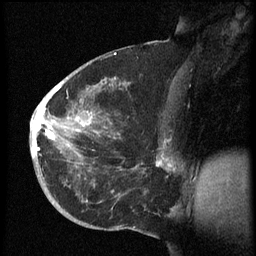
Breast MRI (dynamic contrast-enhanced), one sagittal slice. Dynamic contrast-enhanced series, image 2 of 3 at this slice position (ordered by acquisition). 1.5 T. TE 4.2 ms, TR 8.4 ms. 2.5 mm slice thickness. 256 × 256 image matrix, field of view 200 × 200 mm. Female patient, age 38 years. Case-level facts recorded for this patient, not image findings: setting: breast cancer imaged before/during neoadjuvant chemotherapy; receptor status: HER2-positive.
Annotated regions visible in this slice (semi-automatically segmented with operator editing):
- analysis volume of interest (the breast-tissue region the enhancement analysis was run in; not a lesion): box from (x=31, y=74) to (x=173, y=202) px
- tumour enhancement mask (voxels above the 70 % enhancement threshold inside the analysis volume of interest): (x=31, y=86)–(x=173, y=171)